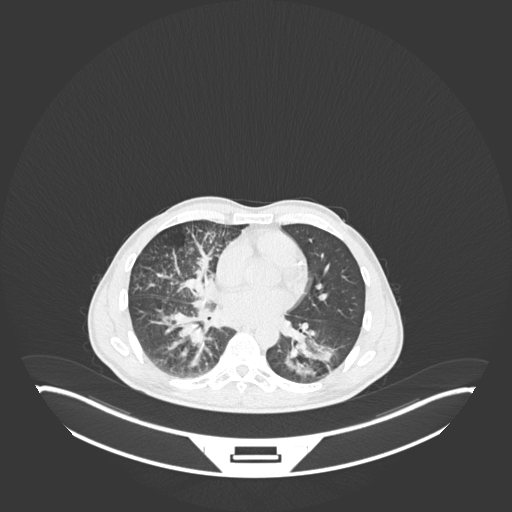
Chest CT, one axial slice. Position 108 of 237 along the scan axis. Reconstruction kernel B30f. 120 kVp. Lung window (W 1500 / L -600 HU). 512 × 512 image matrix, field of view 500 × 500 mm. Patient: male, 49 years. Case-level facts recorded for this patient, not image findings: clinical TNM (as recorded): T2b N1 M0.
Outlined on this slice (rectangle marked by the reading radiologist):
- lung tumour (recorded histology: adenocarcinoma): bounding box (x1, y1, x2, y2) in pixels: (283, 331, 344, 381)